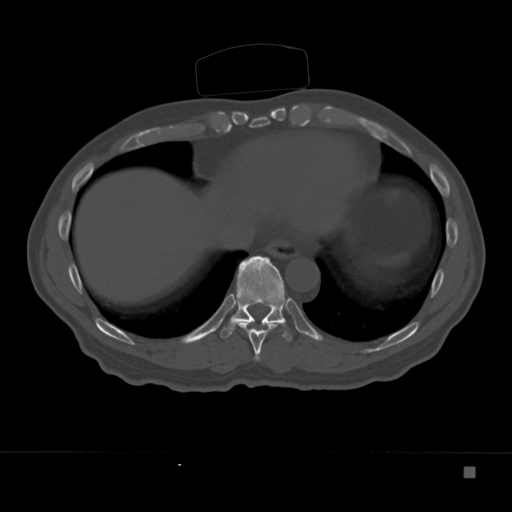
CT including the spine, one axial slice. Position 180 of 332 along the scan axis. 120 kVp. Bone window (W 1800 / L 400 HU). 1.5 mm slice thickness. 512 × 512 image matrix, field of view 389 × 389 mm. Male patient, age 72 years. From the clinical record (not read from this slice): primary cancer: skeletal.
Structures marked on this image (semi-automatic segmentation, software-assisted and operator-edited):
- T10 vertebra: bounding box (x1, y1, x2, y2) in pixels: (220, 256, 292, 341)
- T9 vertebra: (234, 321, 285, 361)